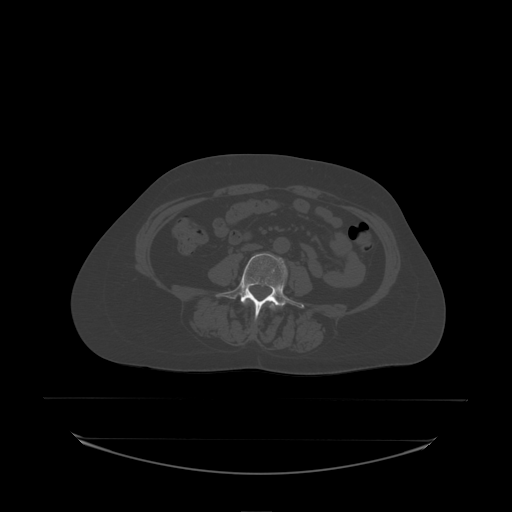
CT including the spine, one axial slice; slice 52 of 242 in the series (ordered by position); bone window (W 1800 / L 400 HU); 512 × 512 image matrix, field of view 500 × 500 mm. Patient: female, 53 years. Case-level facts recorded for this patient, not image findings: primary cancer: lung; vertebrae with lytic lesions (as recorded): T7, L1.
Outlined on this slice (semi-automatic segmentation, software-assisted and operator-edited):
- L3 vertebra: box from (x=268, y=302) to (x=275, y=310) px
- L4 vertebra: (x=216, y=253)–(x=304, y=320)